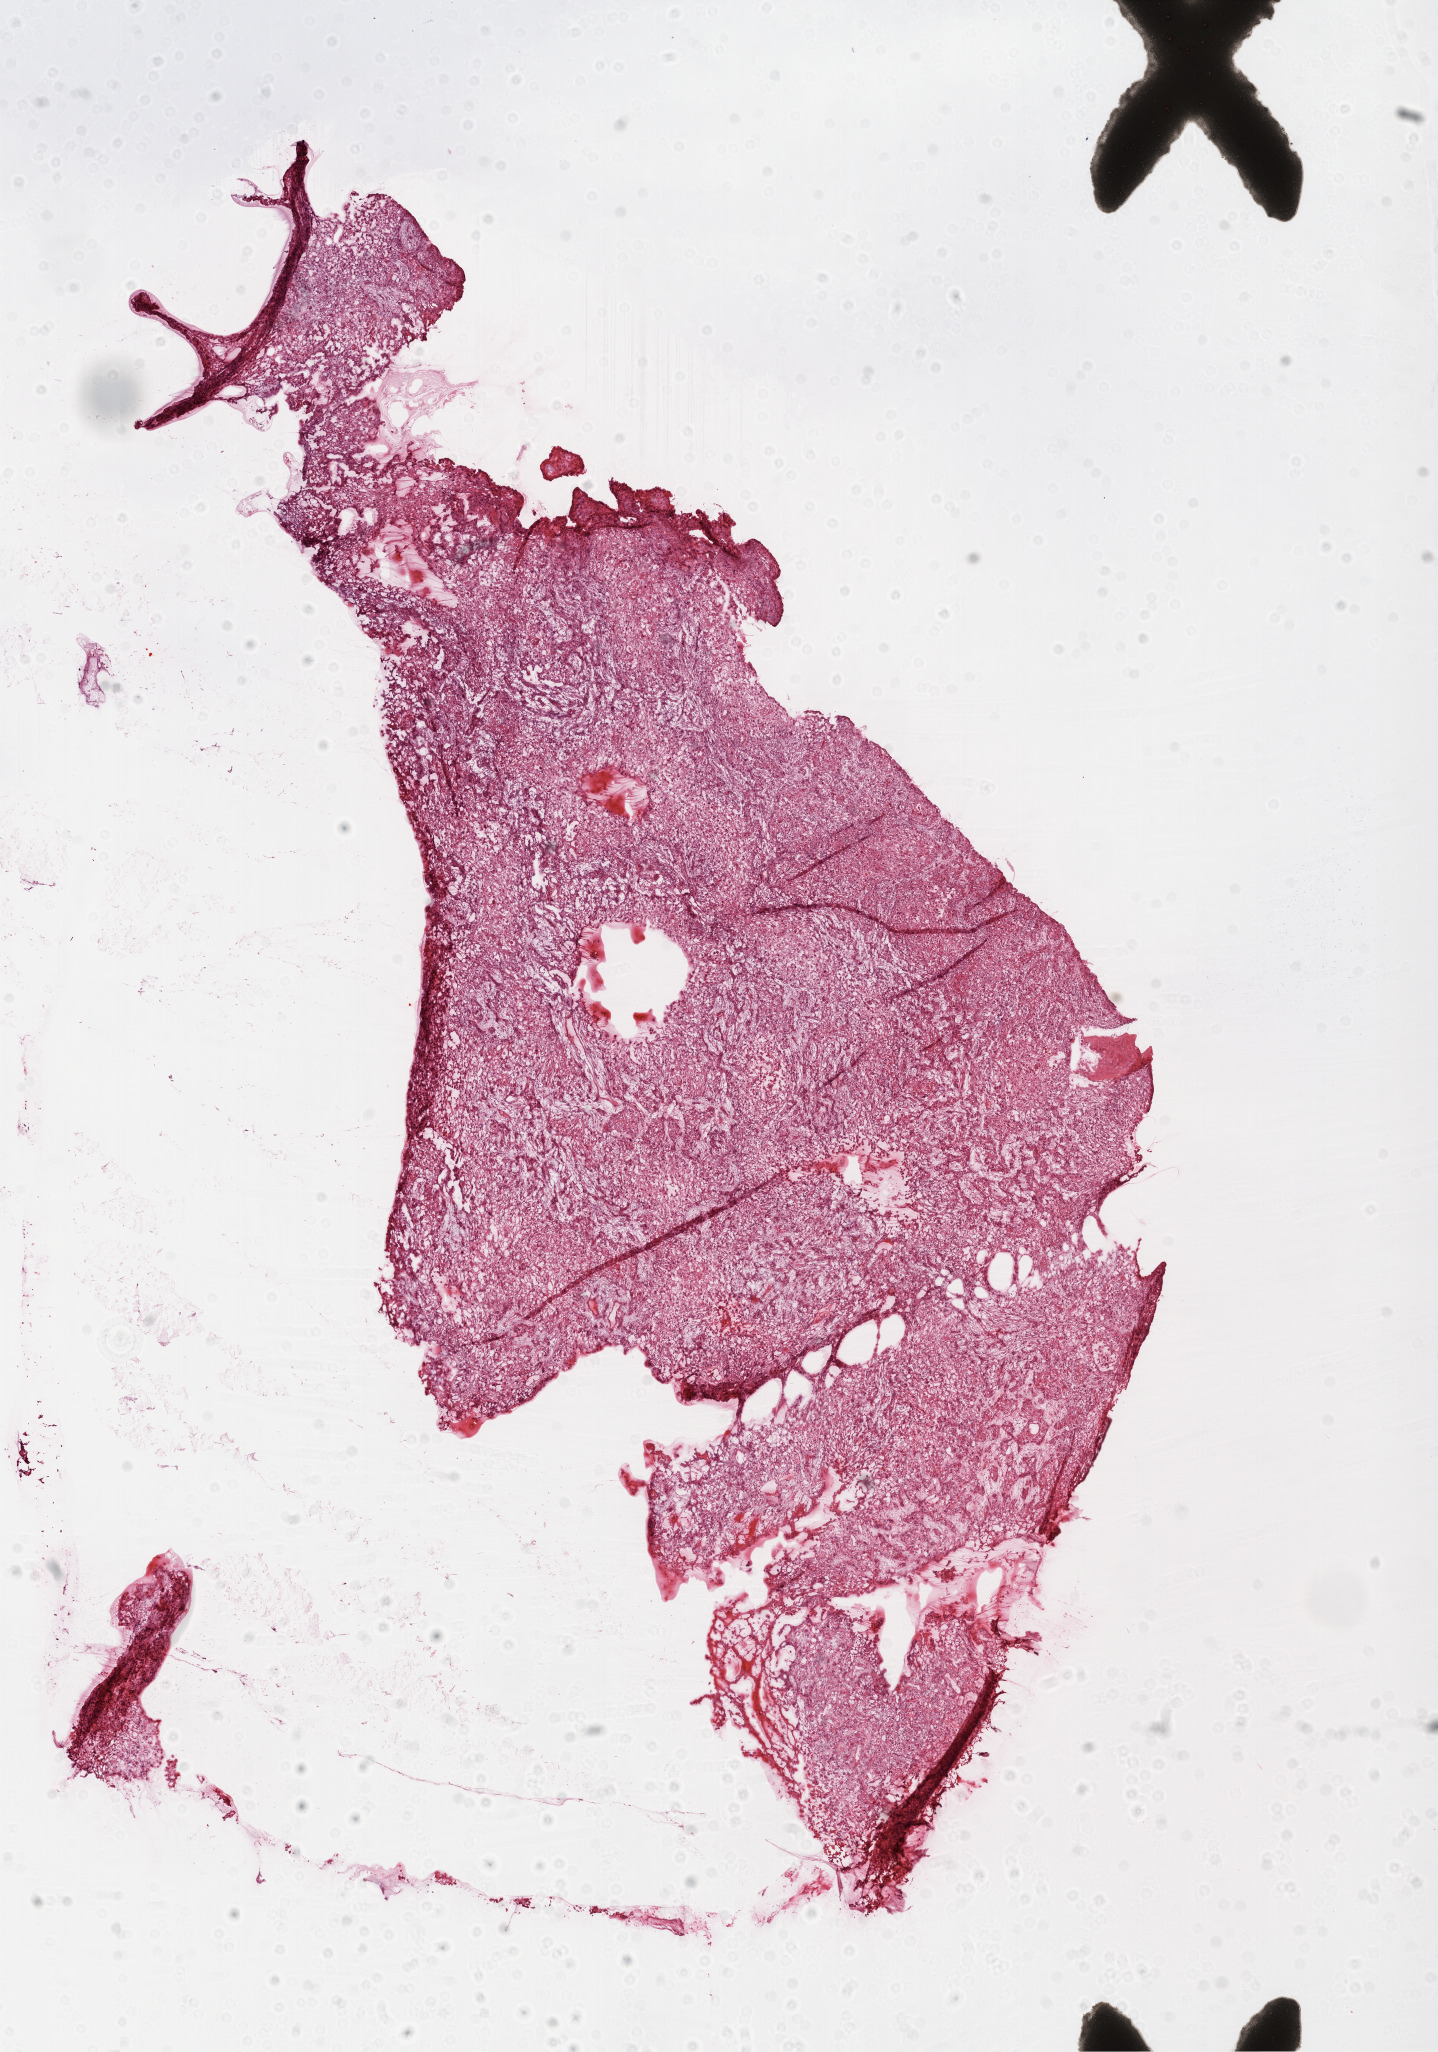
Hematoxylin and eosin (H&E) stained whole-slide image, whole scanned area (about 11.6 x 16.6 mm) shown as a low-resolution overview, frozen section from the top of the tissue portion, sample: primary tumour, lung. Male patient; age at initial diagnosis 71 years. Pathologist review of this section (percent, as recorded): tumour nuclei 90%, necrosis 0%.
TNM: T3 N0 M0. AJCC pathologic stage: IIIA. Diagnosis: Squamous cell carcinoma, NOS (upper lobe, lung).